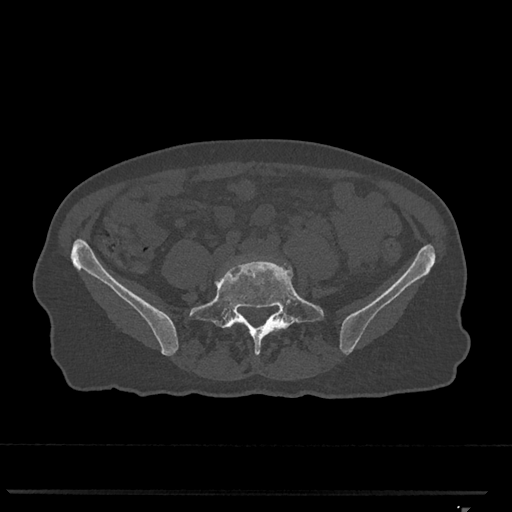
CT including the spine, one axial slice; slice 161 of 793 in the series (ordered by position); 120 kVp; bone window (W 1800 / L 400 HU); 0.5 mm slice thickness; 512 × 512 image matrix. Female patient, age 62 years. From the clinical record (not read from this slice): primary cancer: renal.
Structures marked on this image (semi-automatic segmentation, software-assisted and operator-edited):
- L4 vertebra: bounding box <217,258,257,280> (left, top, right, bottom; pixels)
- L5 vertebra: <189,258,324,355>